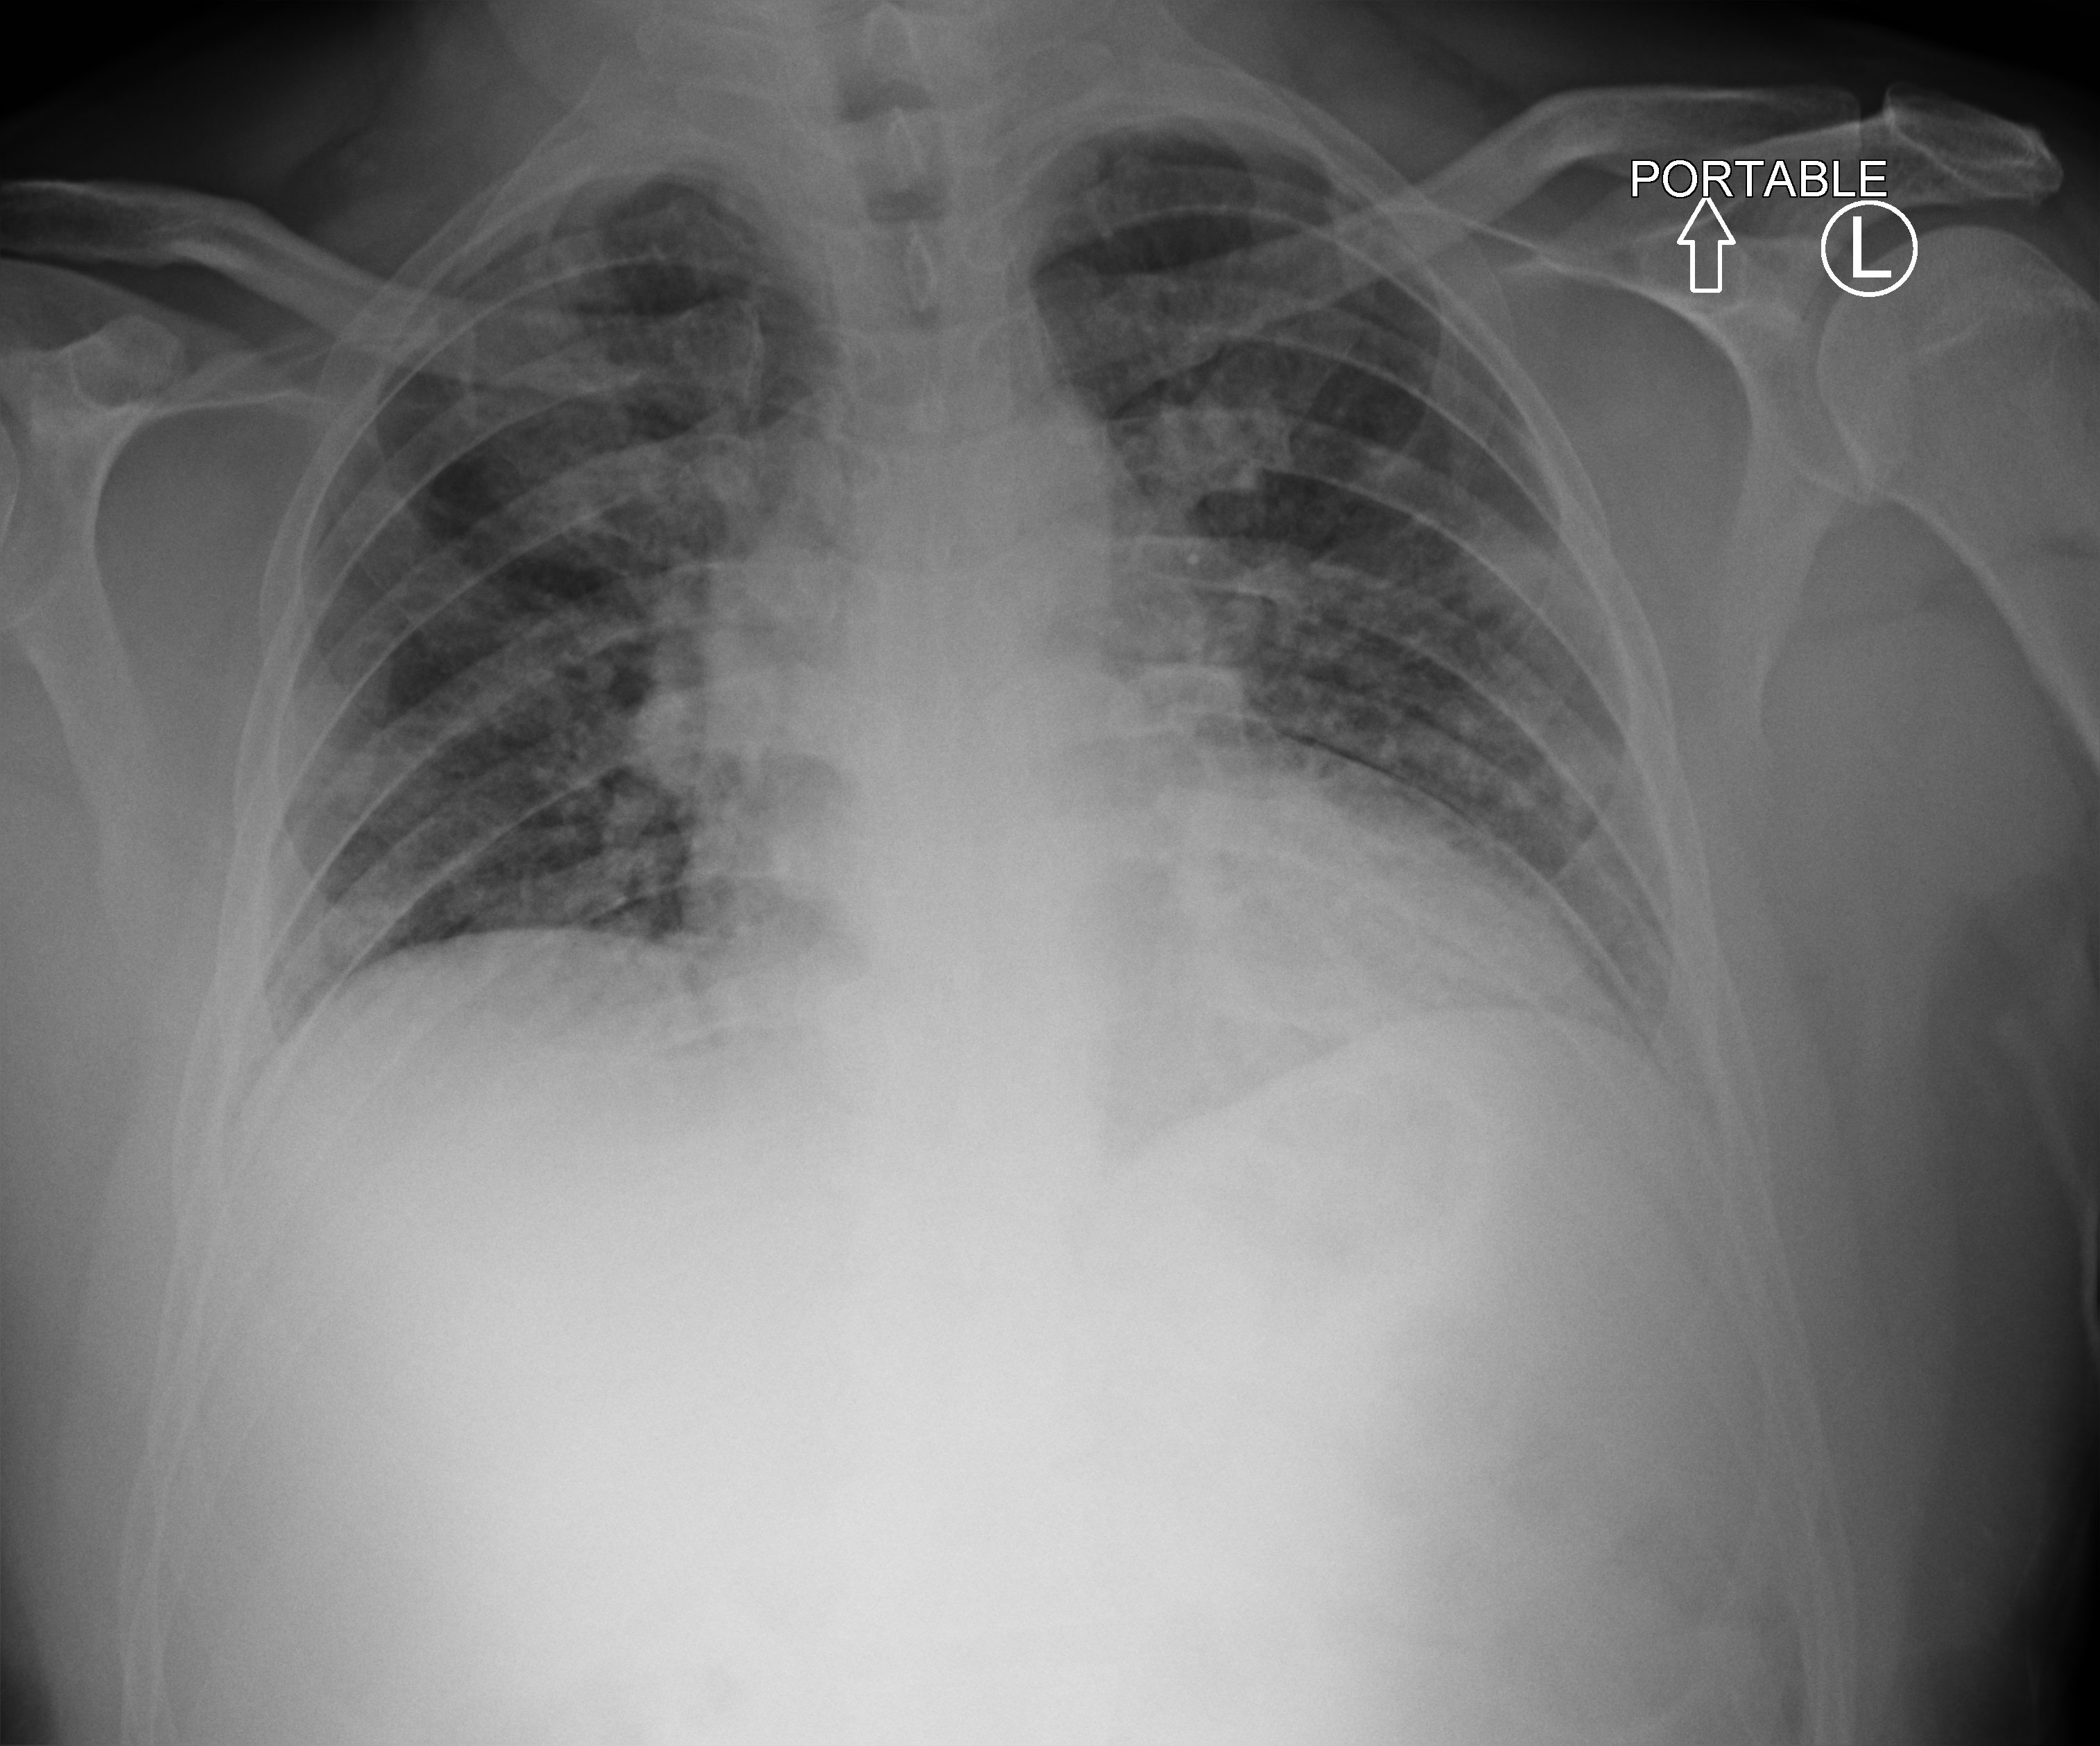
Portable chest radiograph. Patient hospitalised with COVID-19; male, aged 18–59 years.
From the hospital-stay record, not from the radiograph (when in the stay this image was taken is not recorded): admitted to intensive care during this hospital stay: no; mechanically ventilated during this hospital stay: yes.